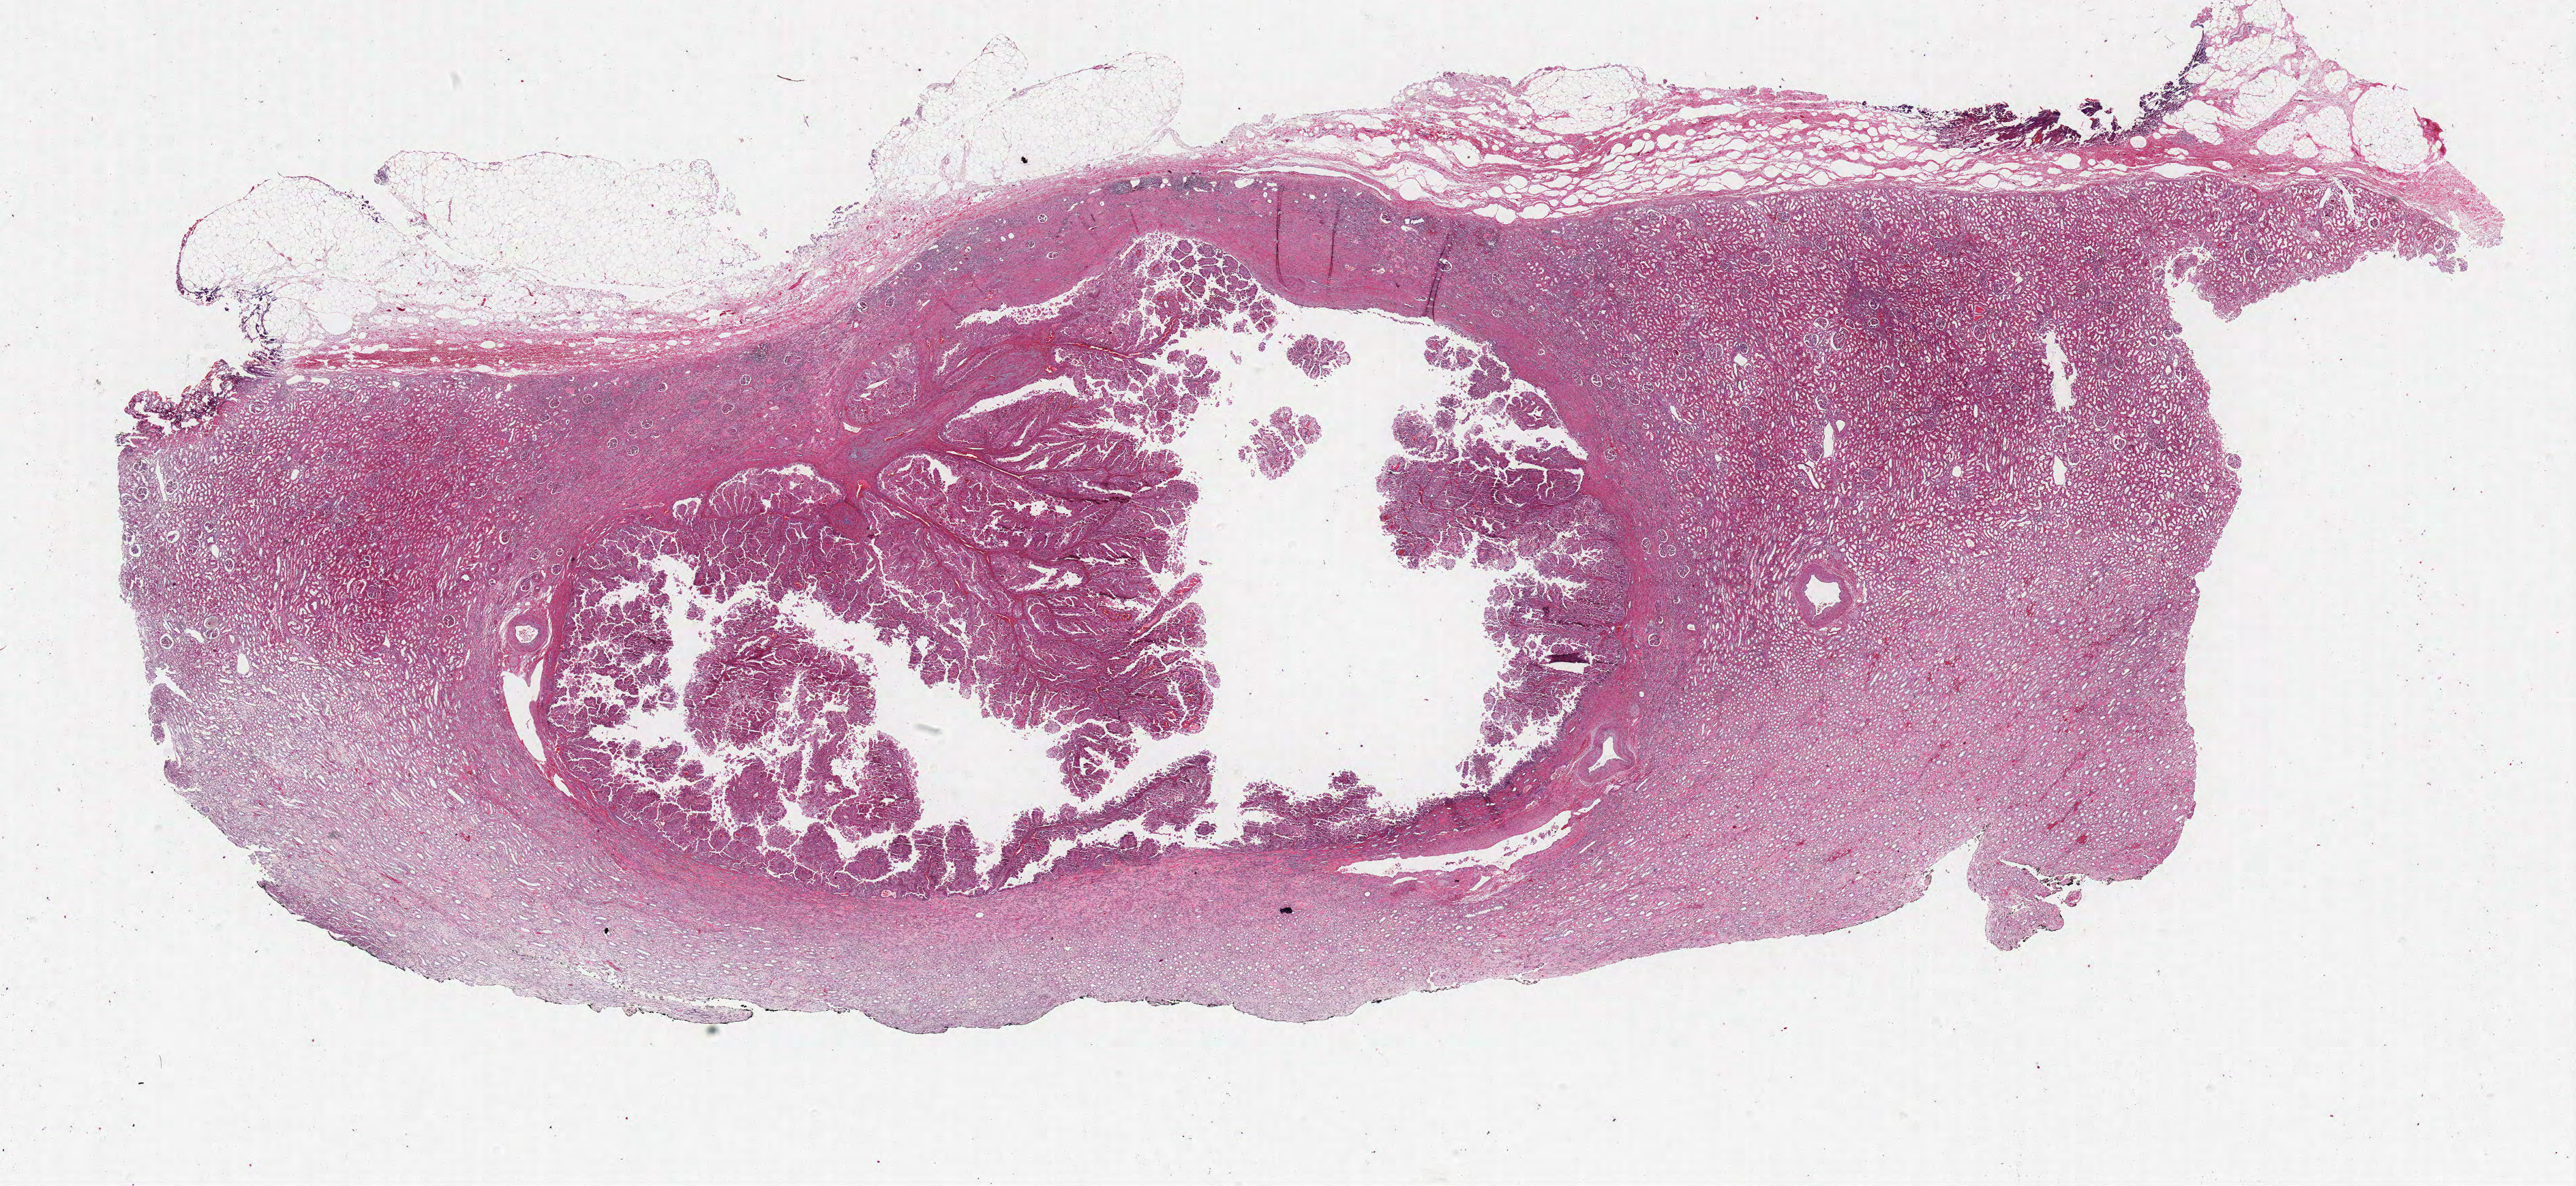
Digitized H&E-stained tissue section (whole slide) — low-resolution overview of the scanned area, about 30.2 x 13.9 mm (from a 40x scan); formalin-fixed paraffin-embedded (FFPE) diagnostic section; sample: primary tumour, kidney. Male patient; age at initial diagnosis 75 years.
Diagnosis: Papillary adenocarcinoma, NOS.